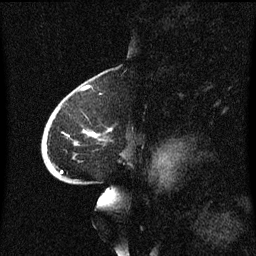
Breast MRI (dynamic contrast-enhanced), one sagittal slice; slice 40 of 60 in the series (ordered by position); dynamic contrast-enhanced series, image 2 of 3 at this slice position (ordered by acquisition); 1.5 T; TE 4.2 ms, TR 8.4 ms; 2 mm slice thickness; 256 × 256 image matrix, field of view 200 × 200 mm. Patient: female, 68 years. From the clinical record (not read from this slice): setting: breast cancer imaged before/during neoadjuvant chemotherapy; receptor status: triple-negative.
Annotated regions visible in this slice (semi-automatic segmentation, software-assisted and operator-edited):
- analysis volume of interest (the breast-tissue region the enhancement analysis was run in; not a lesion): box from (x=43, y=94) to (x=128, y=173) px
- tumour enhancement mask (voxels above the 70 % enhancement threshold inside the analysis volume of interest): (x=61, y=130)–(x=112, y=173)